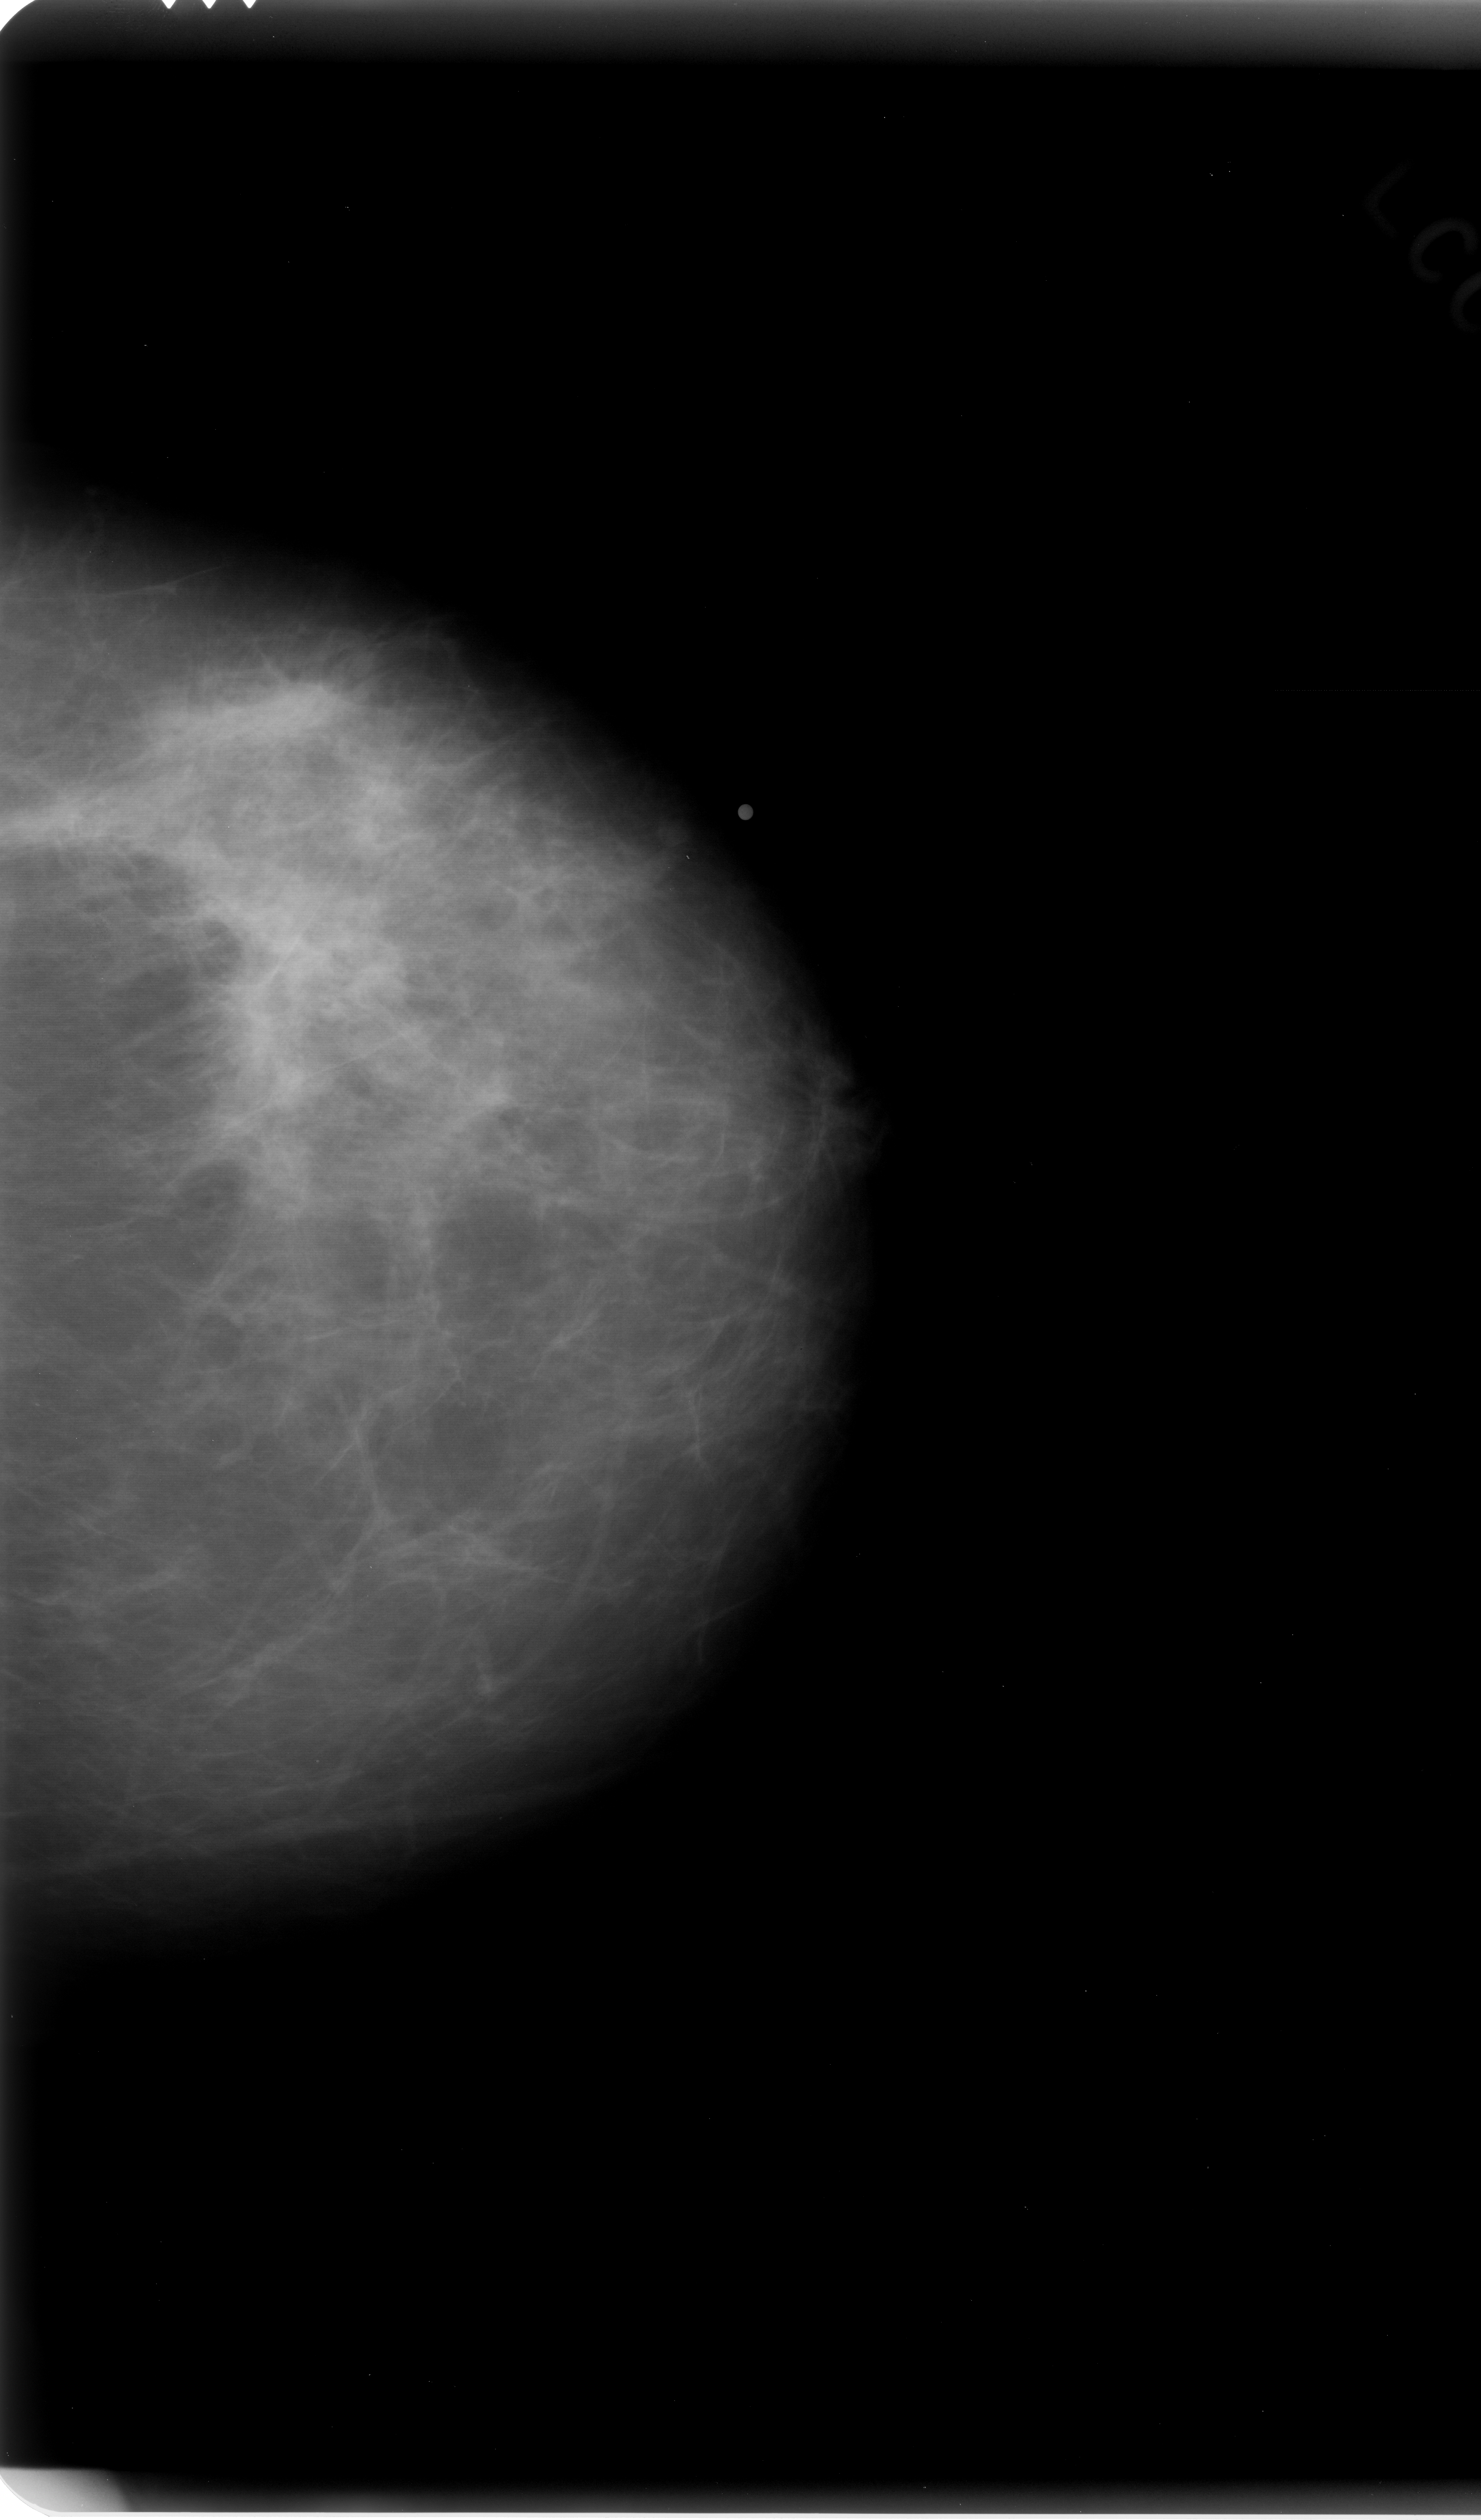
Scanned film-screen mammogram; left breast; CC view; breast composition: almost entirely fatty (BI-RADS density category 1 of 4).
- Mass, shape irregular, margins spiculated; BI-RADS assessment category 5; pathology (as recorded): malignant.